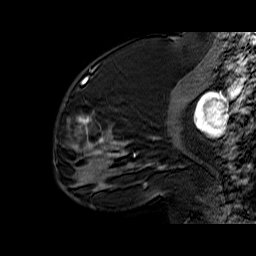
Breast MRI (dynamic contrast-enhanced), one sagittal slice; position 22 of 60 along the scan axis; dynamic contrast-enhanced series, time point 2 of 6 at this slice position (early post-contrast); 1.5 T; TE 6.4 ms, TR 32.9 ms; 4 mm slice thickness; 256 × 256 image matrix, field of view 200 × 200 mm. Female patient. From the clinical record (not read from this slice): setting: breast cancer imaged before/during neoadjuvant chemotherapy; receptor status: triple-negative.
Outlined on this slice (semi-automatically segmented with operator editing):
- analysis volume of interest (the breast-tissue region the enhancement analysis was run in; not a lesion): box from (x=56, y=65) to (x=159, y=174) px
- tumour enhancement mask (voxels above the 100 % enhancement threshold inside the analysis volume of interest): (x=68, y=77)–(x=159, y=170)